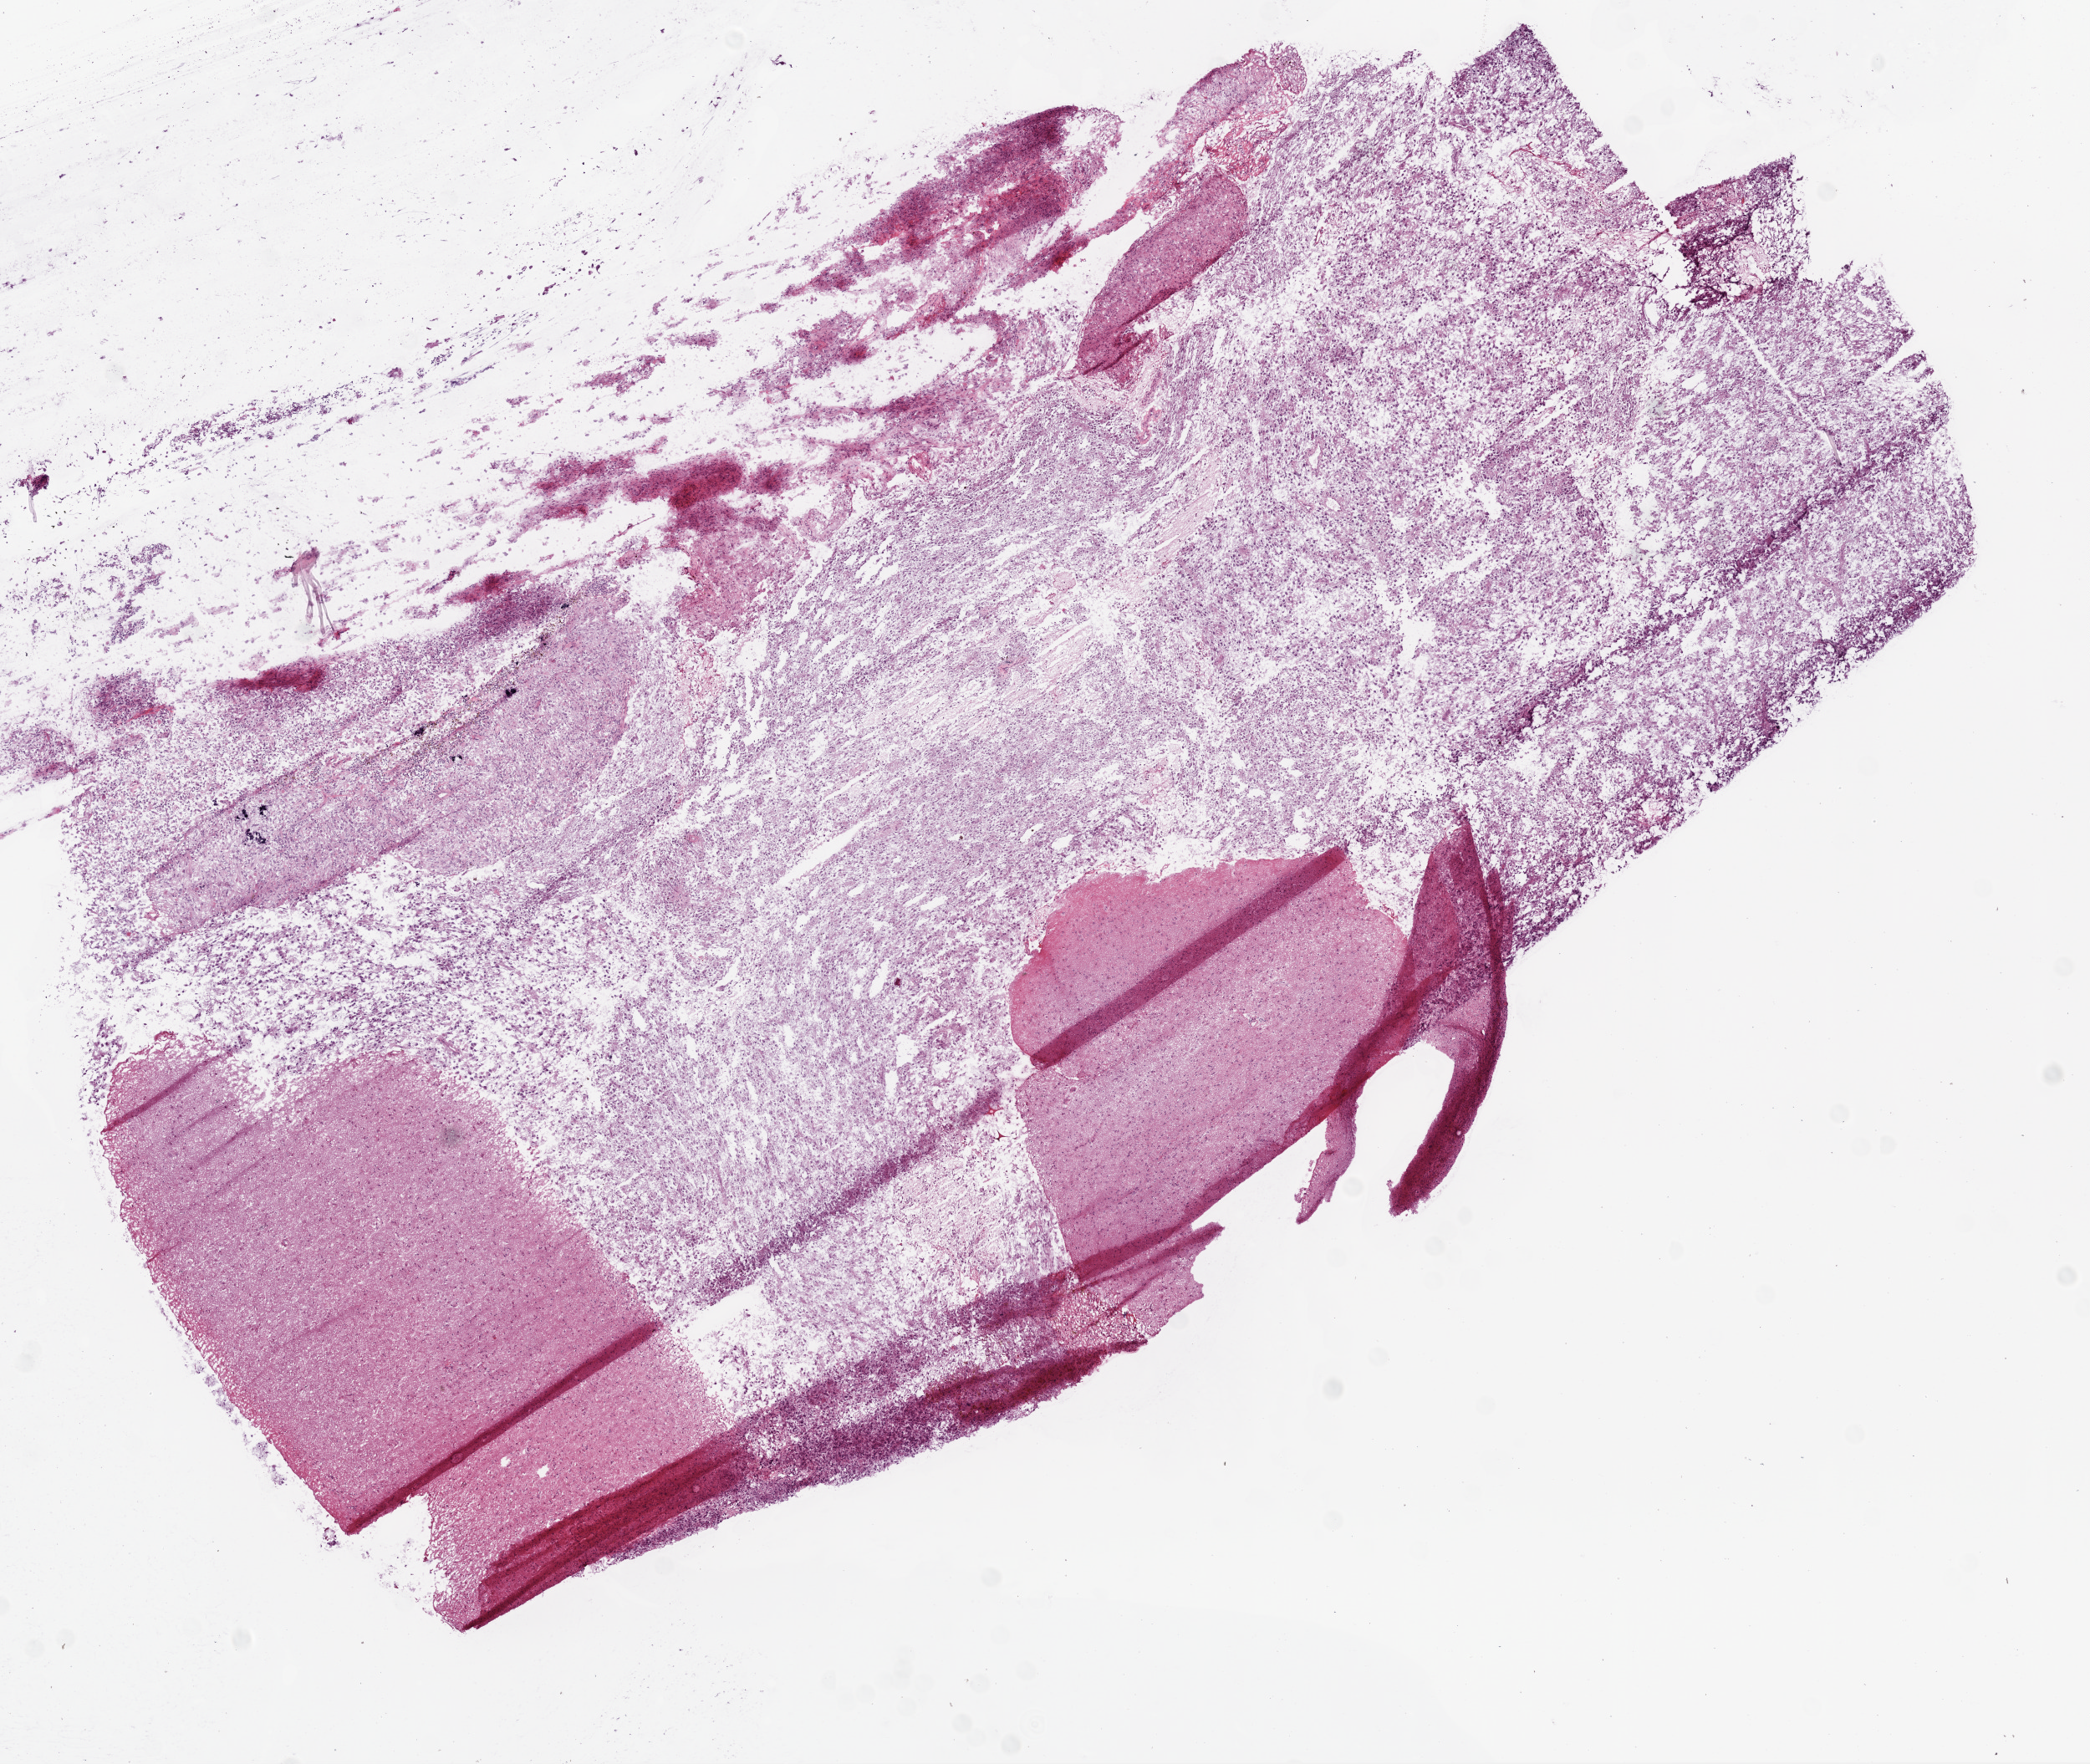
H&E-stained whole-slide image, low-resolution overview of the scanned area, about 10.0 x 8.5 mm (acquisition: 20x scan), frozen section, sample: primary tumour, brain. Male, age 47 years at initial diagnosis. Slide review estimates, as recorded: tumour cells 70%, tumour nuclei 80%.
Pathologic diagnosis: Glioblastoma.